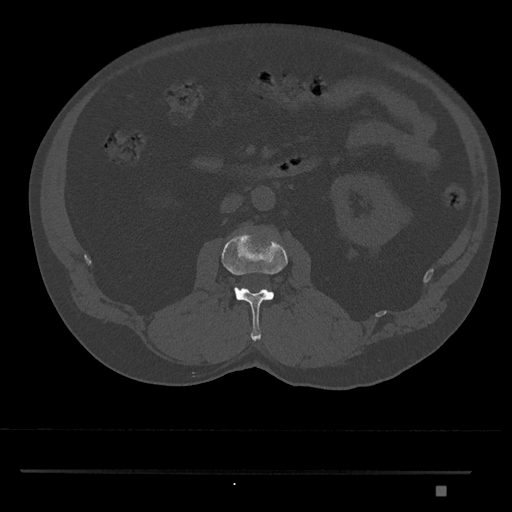
CT including the spine, one axial slice; slice 739 of 1134 in the series (ordered by position); 120 kVp; bone window (W 1800 / L 400 HU); 0.5 mm slice thickness; 512 × 512 image matrix, field of view 429 × 429 mm. Patient: male, 65 years. Case-level facts recorded for this patient, not image findings: primary cancer: prostate.
Outlined on this slice (semi-automatic segmentation, software-assisted and operator-edited):
- L2 vertebra: box from (x=222, y=233) to (x=288, y=341) px